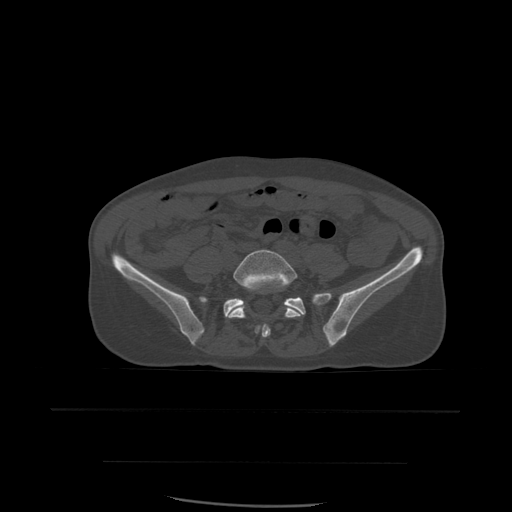
CT including the spine, one axial slice; slice 140 of 574 in the series (ordered by position); bone window (W 1800 / L 400 HU); 1.25 mm slice thickness; 512 × 512 image matrix. Patient age 48 years. From the clinical record (not read from this slice): primary cancer: lung; vertebrae with lytic lesions (as recorded): T11.
Structures marked on this image (semi-automatically segmented with operator editing):
- L5 vertebra: box from (x=229, y=250) to (x=304, y=338) px